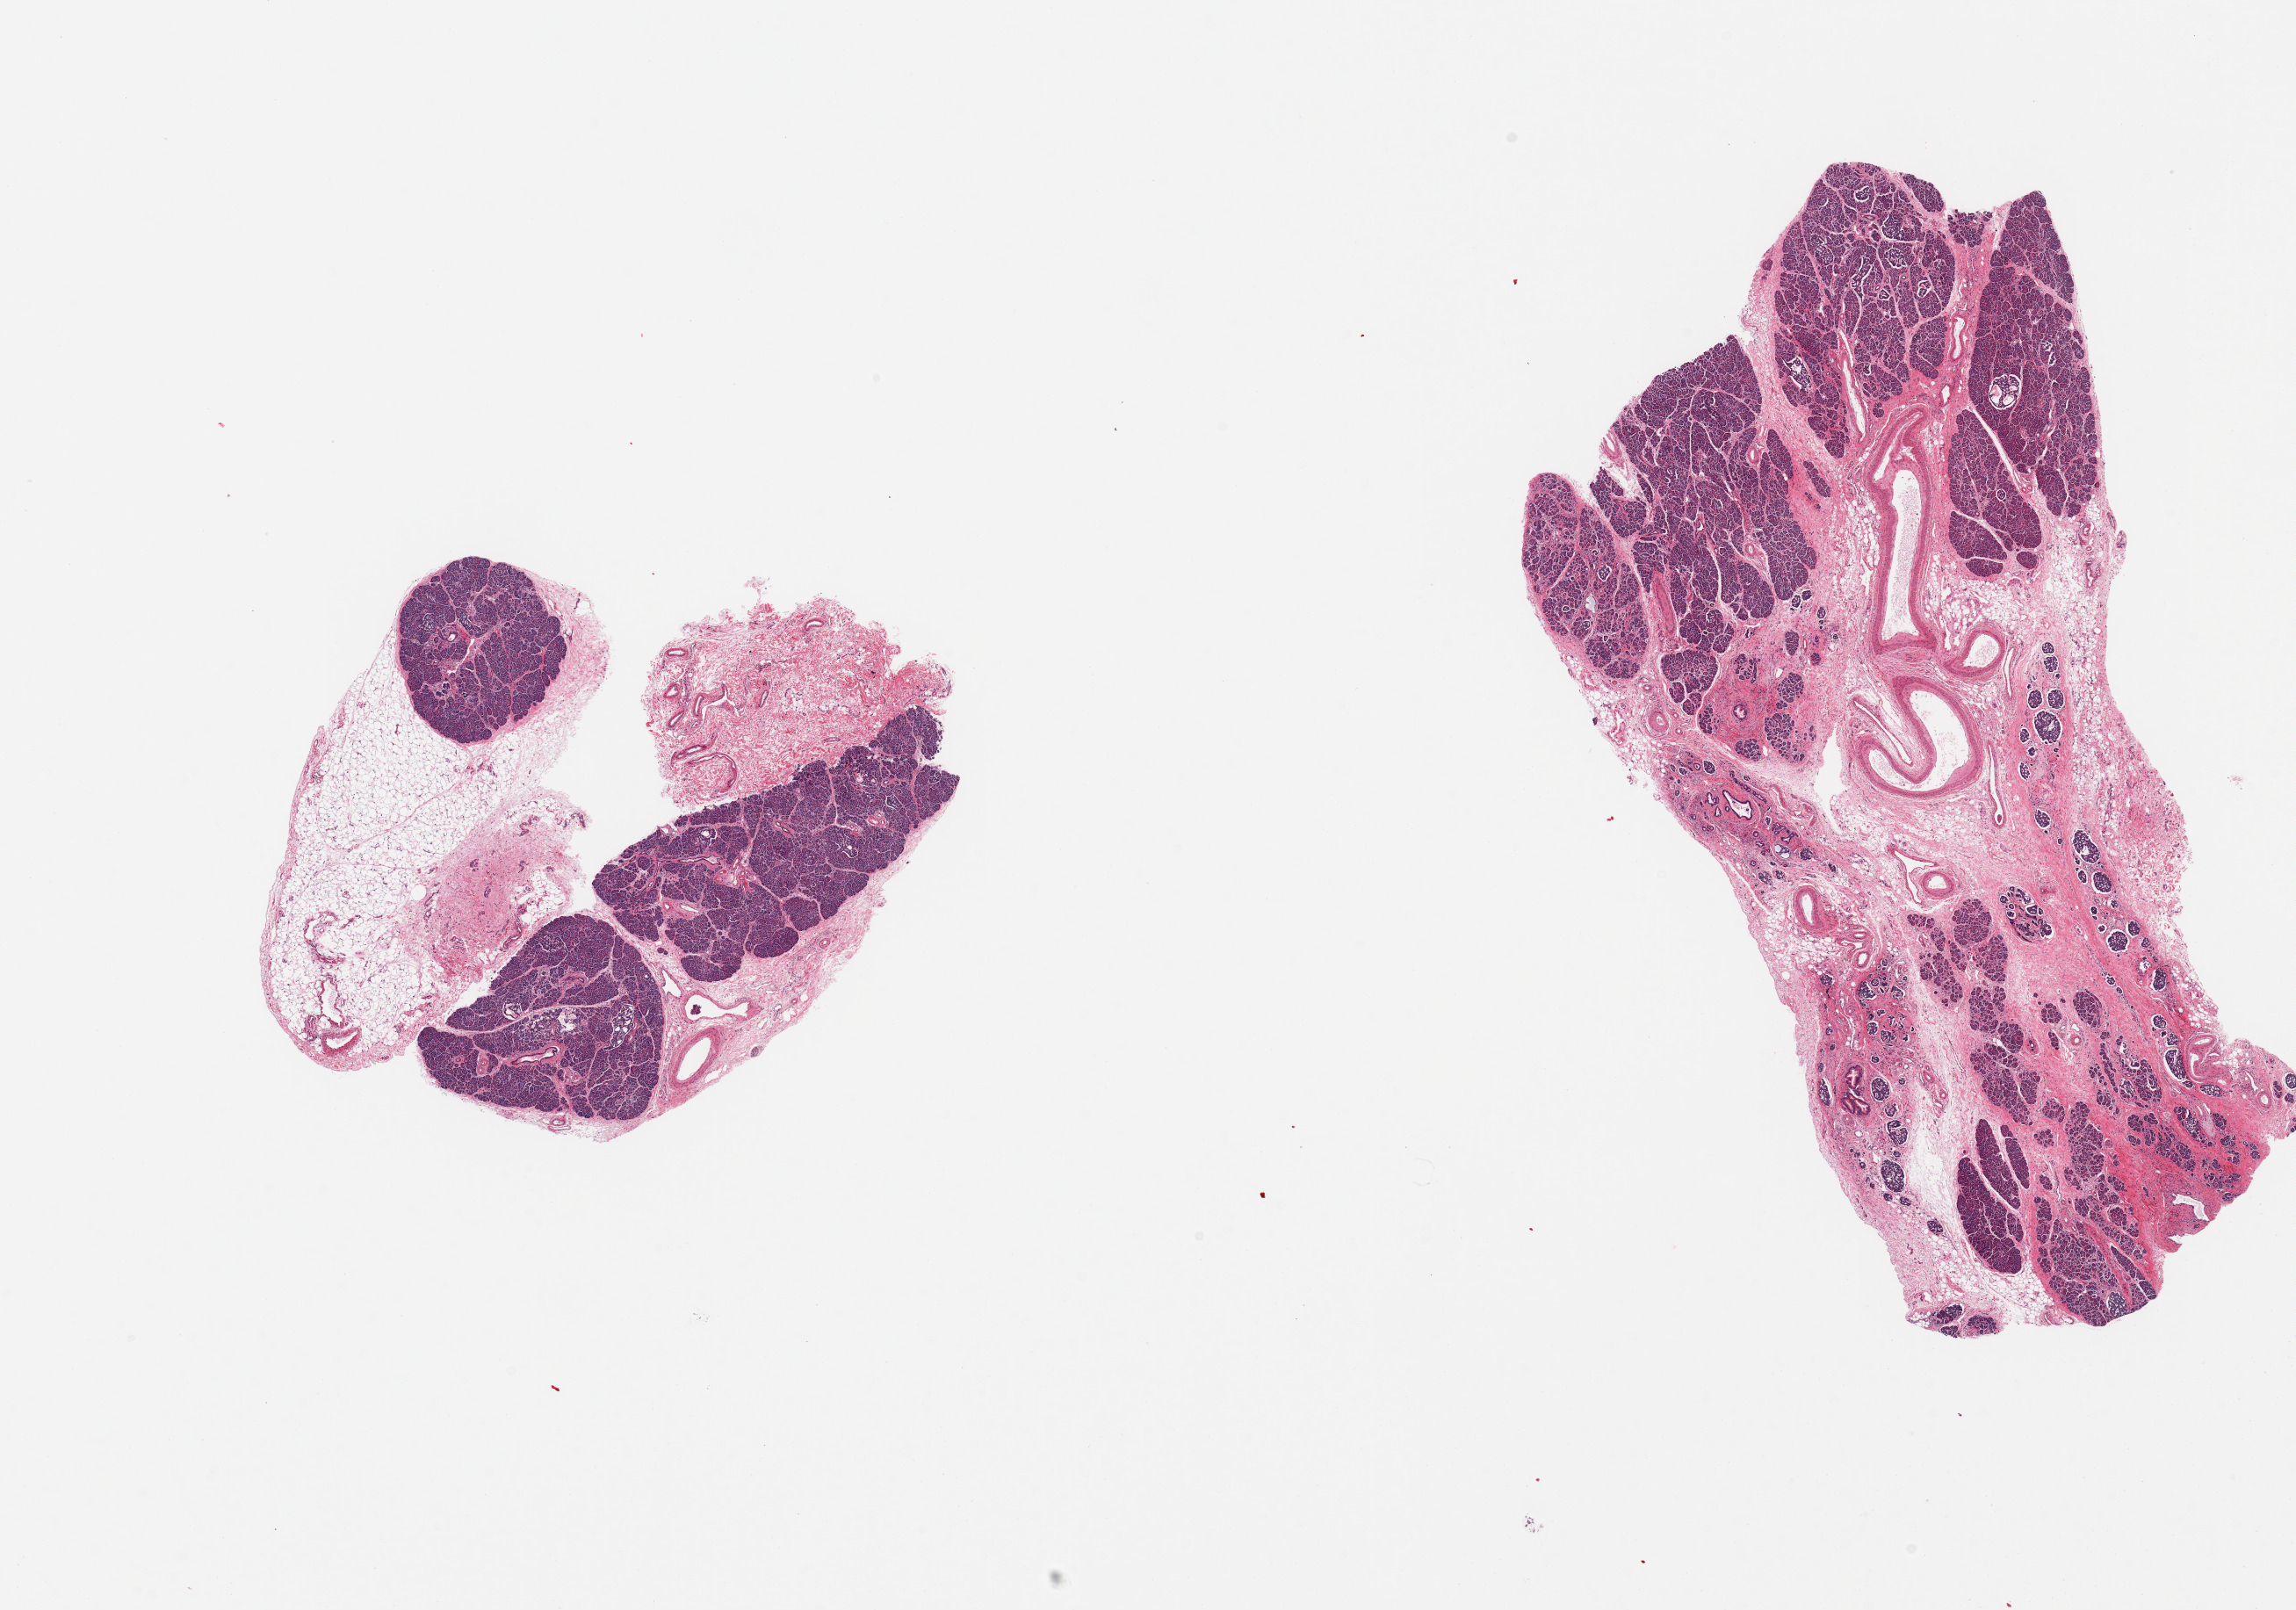
Digitized haematoxylin and eosin-stained section — a low-resolution overview of the entire scanned area, about 20.7 x 14.5 mm. PAXgene-fixed, paraffin-embedded tissue. Target tissue: pancreas. Tissue donor sample. Female donor.
* review note (as recorded): 2 pieces; well preserved; moderate fibrosis and loss of exocrine tissue